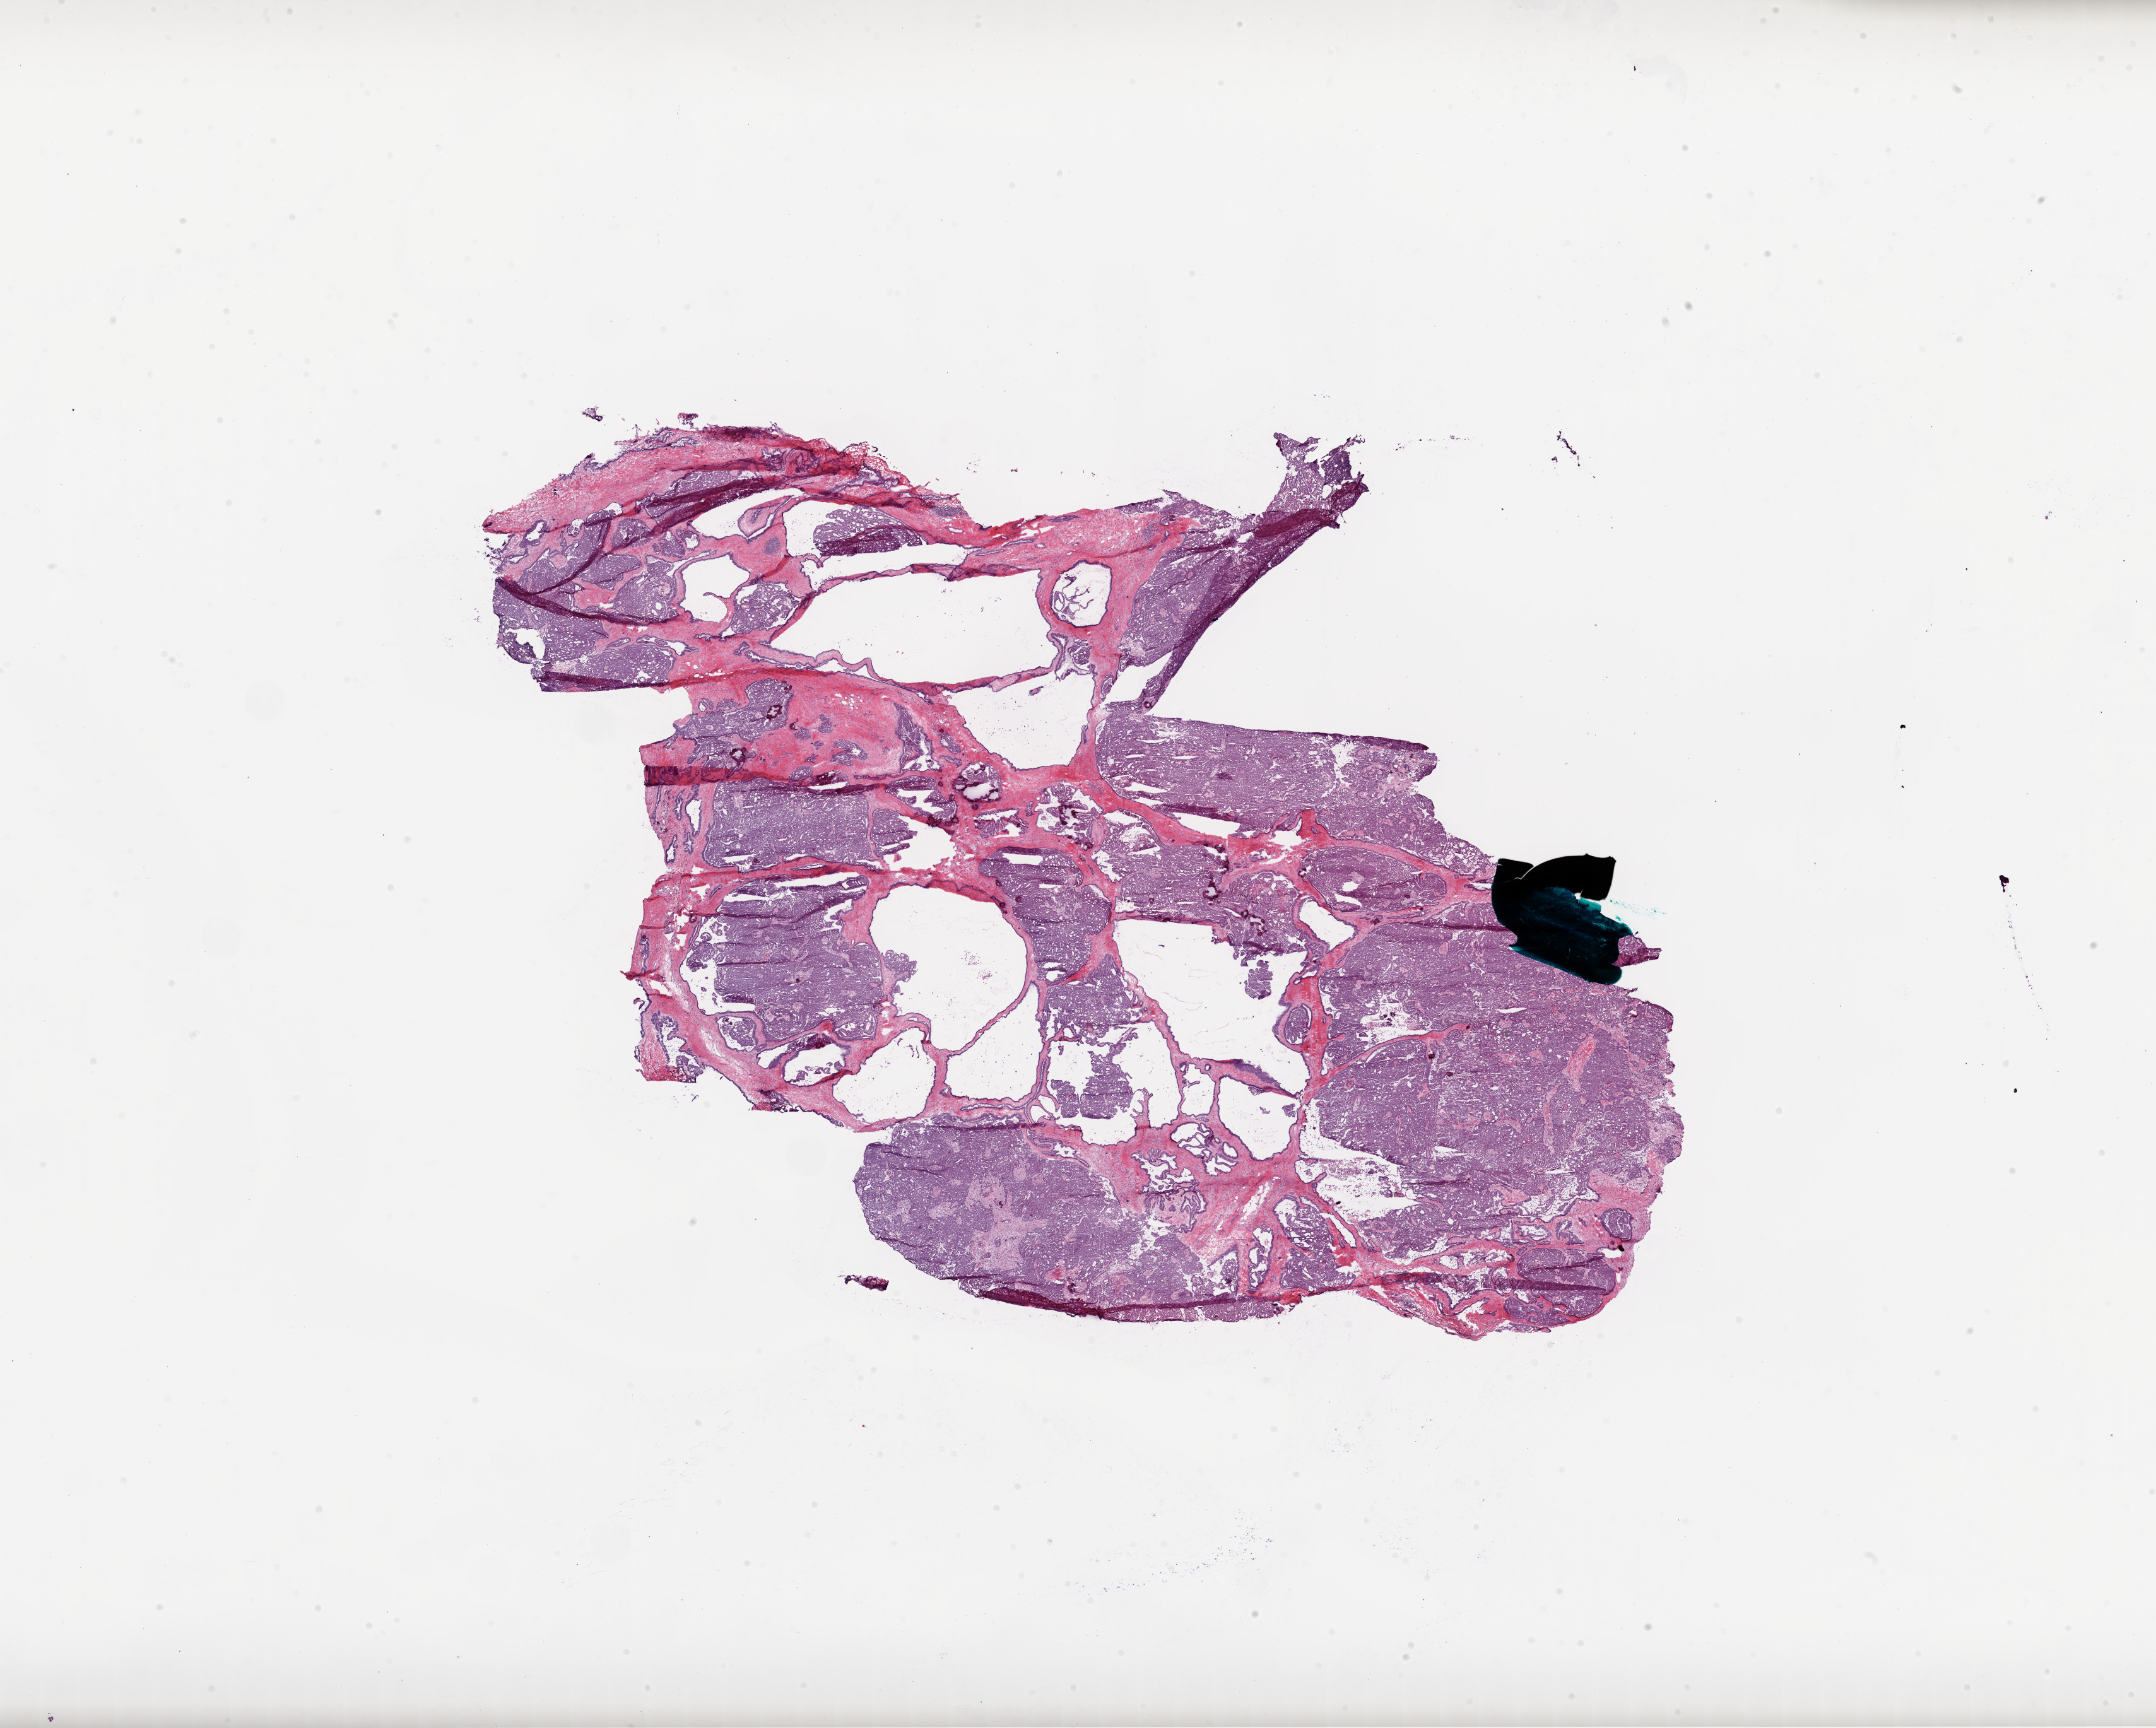
H&E-stained whole-slide image — whole scanned area (about 27.6 x 22.1 mm, acquisition: 20x scan) shown as a low-resolution overview. Frozen section. Primary tumour sample from the ovary. Female patient; age at initial diagnosis 59 years. Histologic grade: G2 (moderately differentiated). Pathologist review of this section (percent, as recorded): tumour cells 69%, tumour nuclei 80%, normal cells 30%, stromal cells 0%, necrosis 1%.
• pathologic diagnosis: Serous cystadenocarcinoma, NOS
• FIGO stage: IIIC